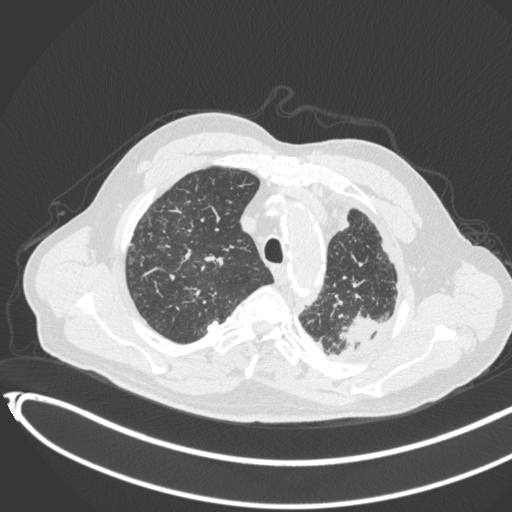
Chest CT, one axial slice. Slice 343 of 451 in the series (ordered by position). Lung window (W 1500 / L -600 HU). 1 mm slice thickness. 512 × 512 image matrix. Patient: male, 78 years. From the clinical record (not read from this slice): clinical TNM (as recorded): T1c N0 M1.
Annotated regions visible in this slice (bounding box drawn by a radiologist):
- lung tumour (recorded histology: adenocarcinoma): bounding box <333,312,386,347> (left, top, right, bottom; pixels)